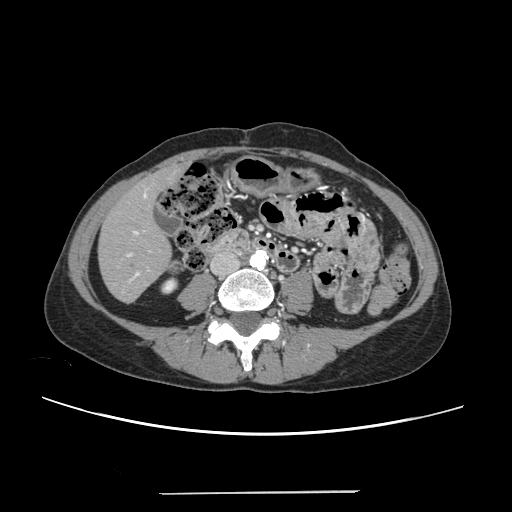
Contrast-enhanced abdominal CT, one axial slice. Position 59 of 240 along the scan axis. 120 kVp. Intravenous contrast given. Soft-tissue window (W 400 / L 40 HU). 512 × 512 image matrix. Female patient, age 60 years. From the clinical record (not read from this slice): diagnosis: colorectal cancer liver metastases, imaged before liver resection; multiple liver metastases: no; largest metastasis: 1.5 cm; disease in both lobes: no.
Annotated regions visible in this slice (manually delineated by an expert):
- liver: bounding box (x1, y1, x2, y2) in pixels: (100, 168, 181, 302)
- planned liver remnant (the part of the liver to remain after resection): (99, 172, 172, 302)
- portal vein (with intrahepatic branches): (127, 188, 149, 277)